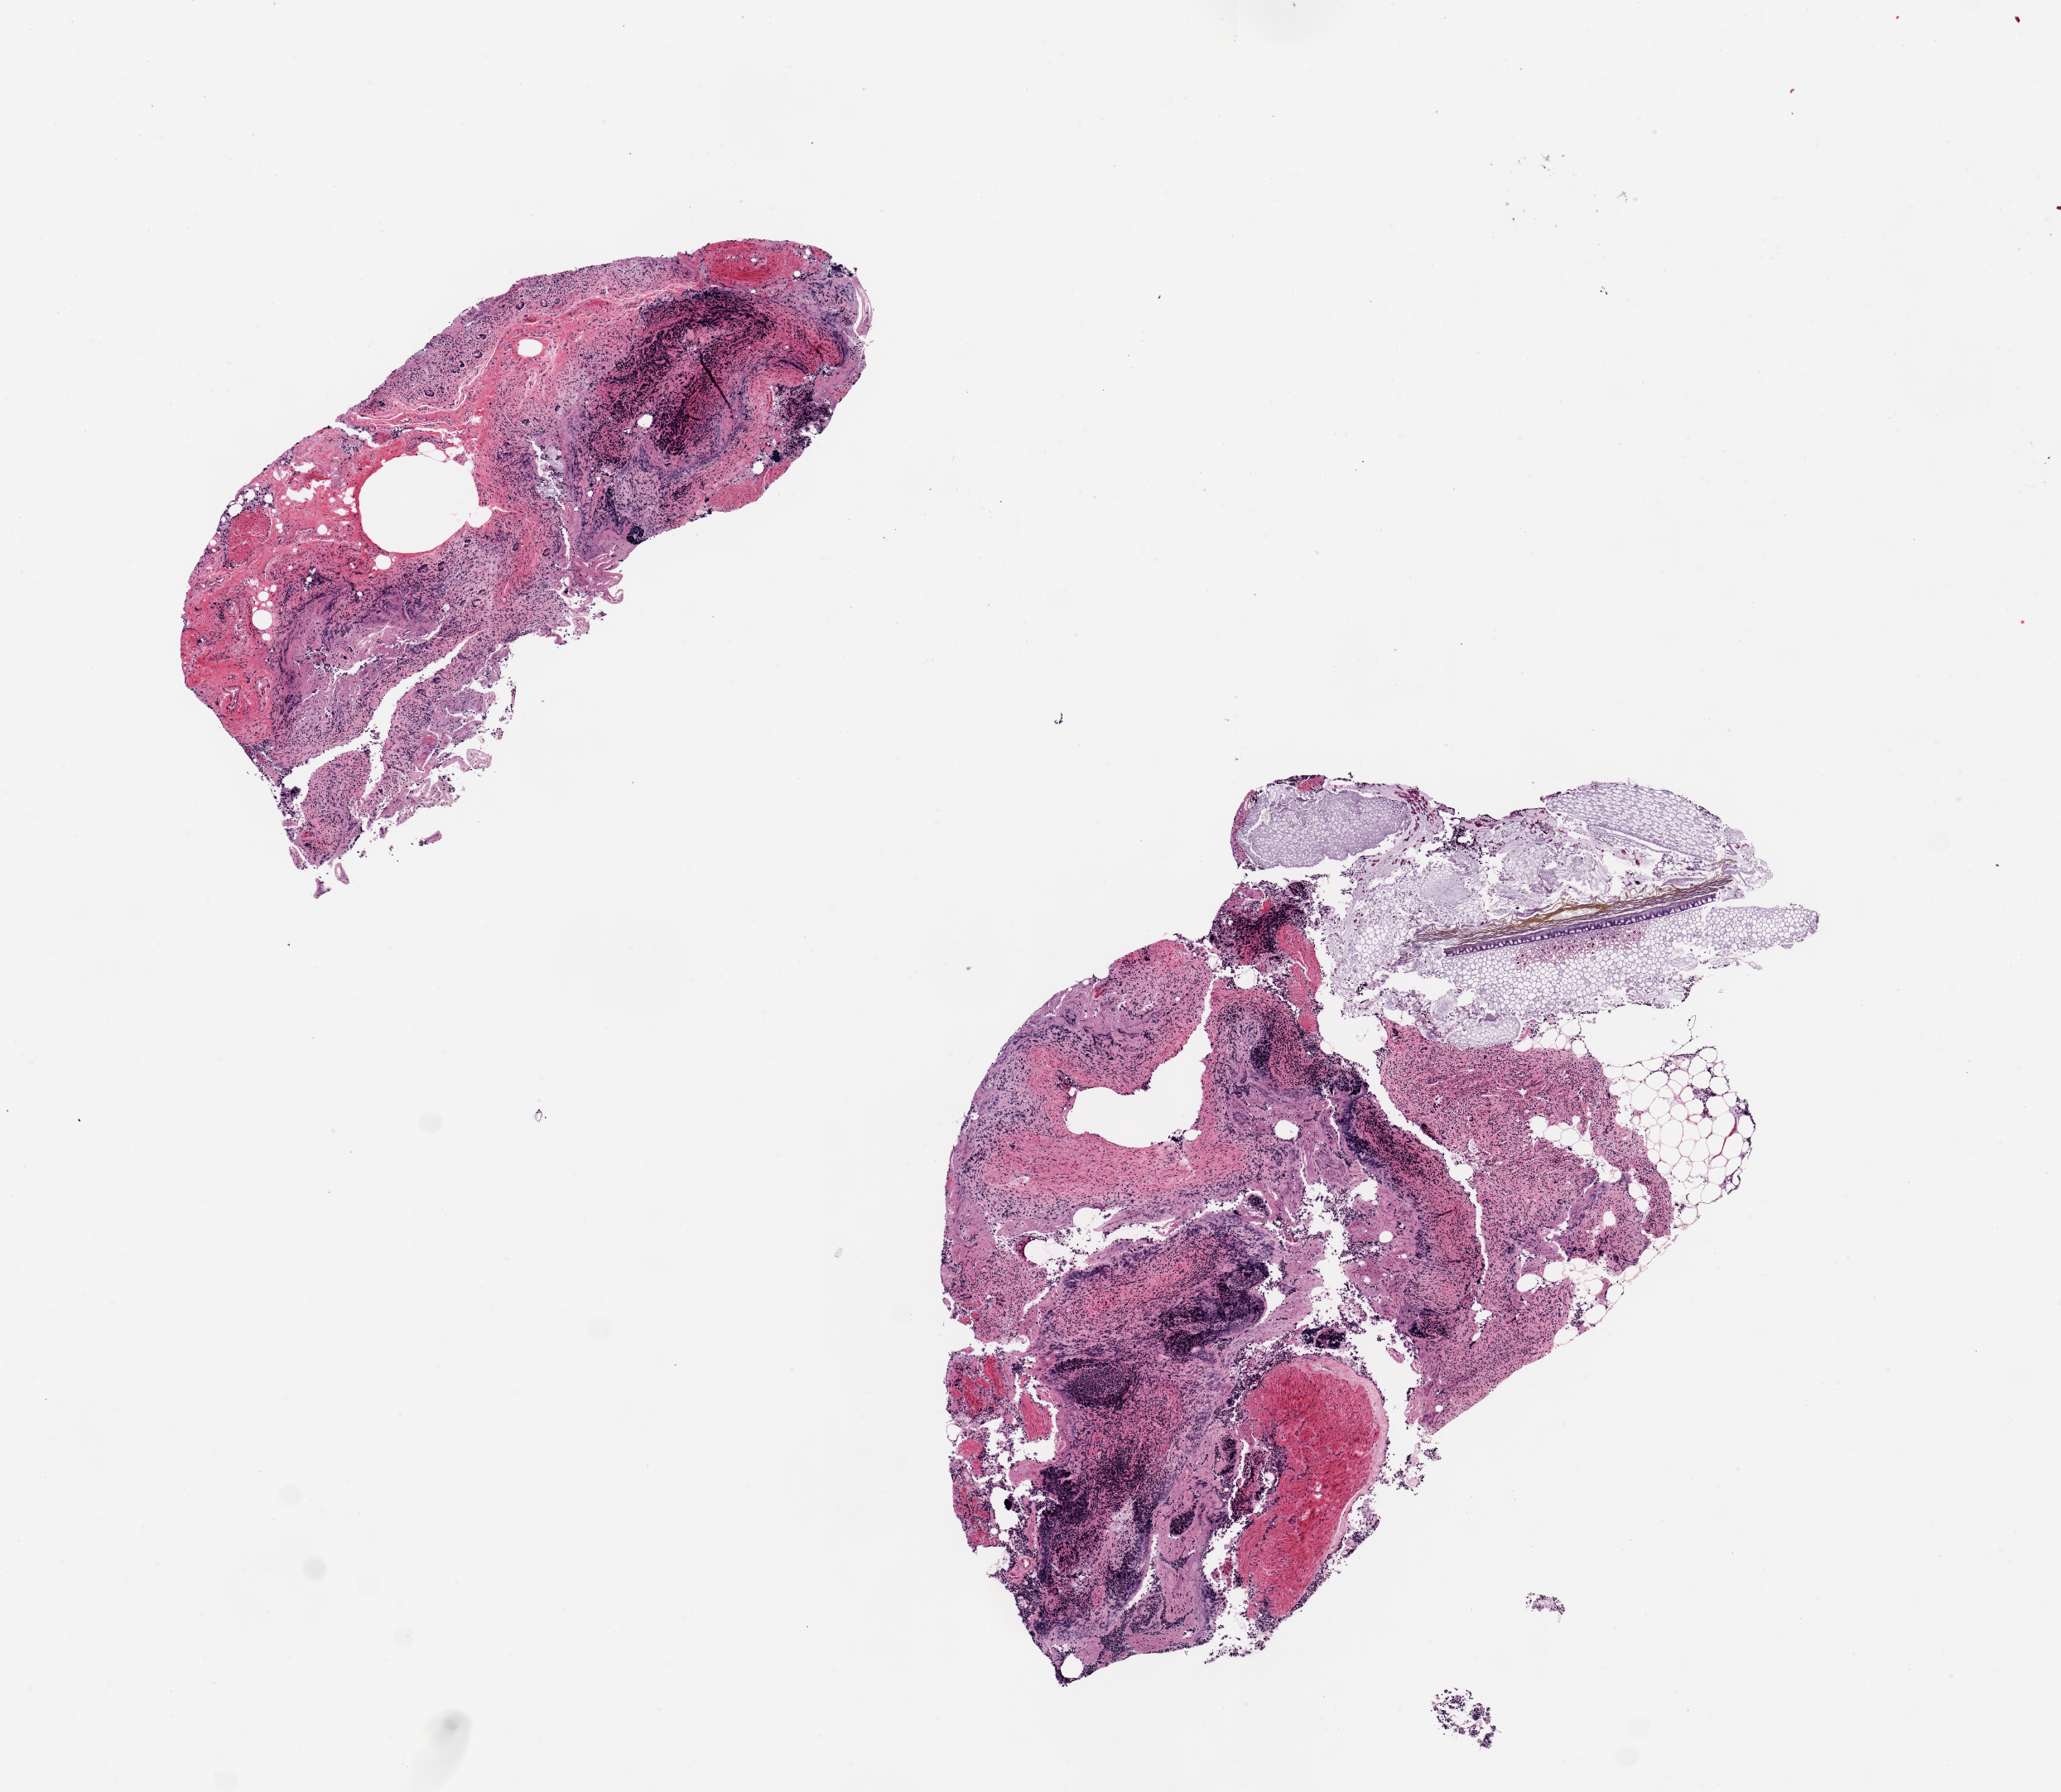
H&E whole-slide image, brightfield — shown as a low-resolution overview of the whole scanned area (about 9.8 x 8.6 mm). PAXgene-fixed, paraffin-embedded tissue. Section of ileum (target tissue). Donor tissue sample. Donor sex: female.
• review note (as recorded): 2 pieces ~4x3mm; Badly autolyzed, ~10% lymphoid element, rest autolyzed mucosa, fragment of fecal elements